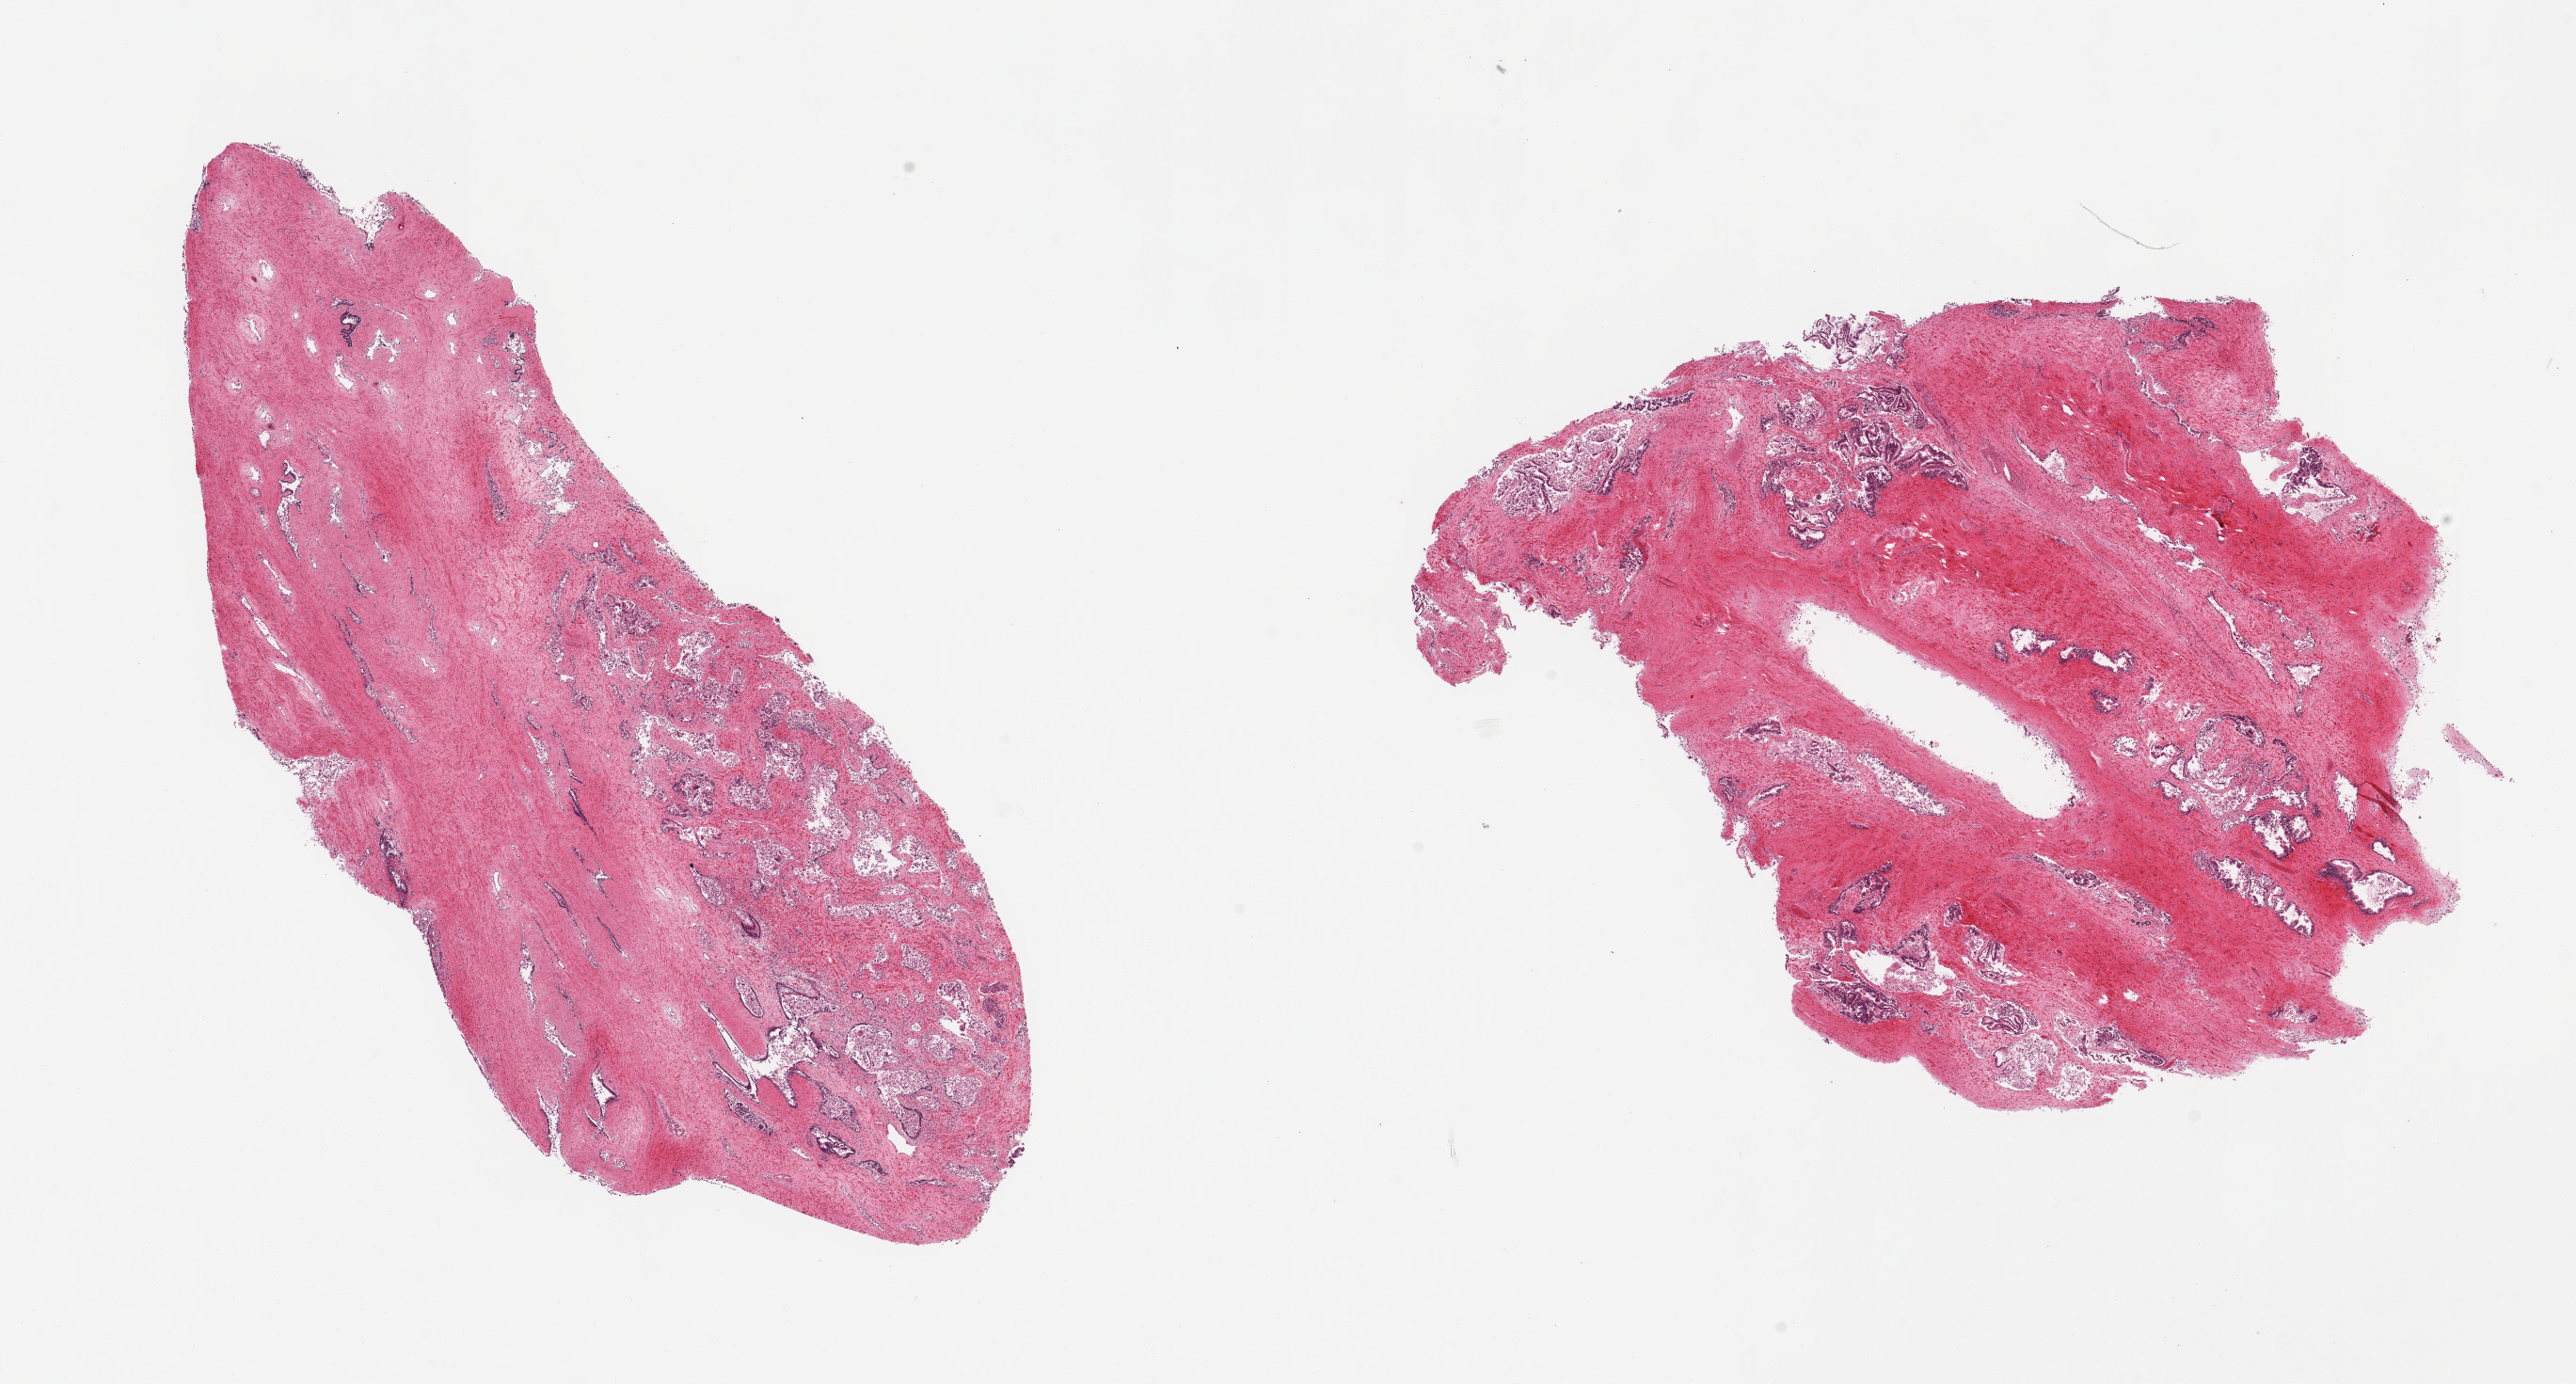
Whole-slide image, H&E stain — shown as a low-resolution overview of the whole scanned area (about 21.7 x 11.6 mm, acquisition: 20x scan); PAXgene-fixed paraffin-embedded (PFPE) section; sampled site (target tissue): prostate; tissue donor sample.
Pathologist's review note for this sample: 2 pieces, glandluar elements with advanced autolysis.